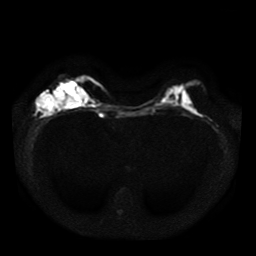
Breast MRI, one axial slice; slice 14 of 41 in the series (ordered by position); diffusion-weighted series; image 2 of 4 stored at this slice position (different b-values; order by instance number); 1.5 T; 5 mm slice thickness; 256 × 256 image matrix, field of view 330 × 330 mm. Female patient.
Structures marked on this image (manually delineated by an expert):
- tumour on diffusion-weighted imaging: bounding box (x1, y1, x2, y2) in pixels: (38, 91, 64, 114)